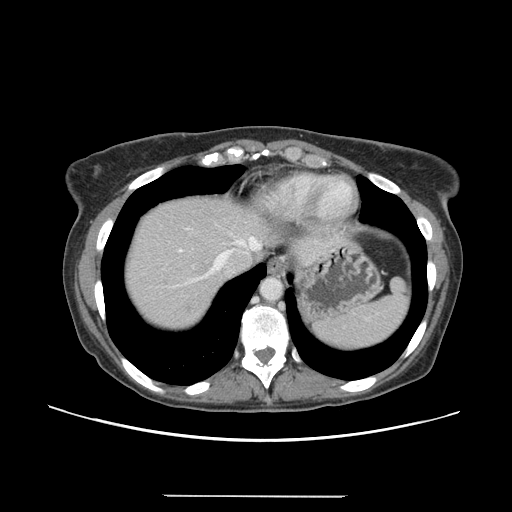
Contrast-enhanced abdominal CT, one axial slice. Slice 126 of 144 in the series (ordered by position). Intravenous contrast given. Soft-tissue window (W 400 / L 40 HU). 512 × 512 image matrix, field of view 380 × 380 mm. Female patient, age 53 years. Case-level facts recorded for this patient, not image findings: diagnosis: colorectal cancer liver metastases, imaged before liver resection; multiple liver metastases: yes; largest metastasis: 1.1 cm; disease in both lobes: no.
Outlined on this slice (outlined manually by an expert reader):
- hepatic veins: bounding box <206,237,261,276> (left, top, right, bottom; pixels)
- liver: <124,197,270,329>
- planned liver remnant (the part of the liver to remain after resection): <124,195,265,294>
- liver metastasis: <186,305,193,315>